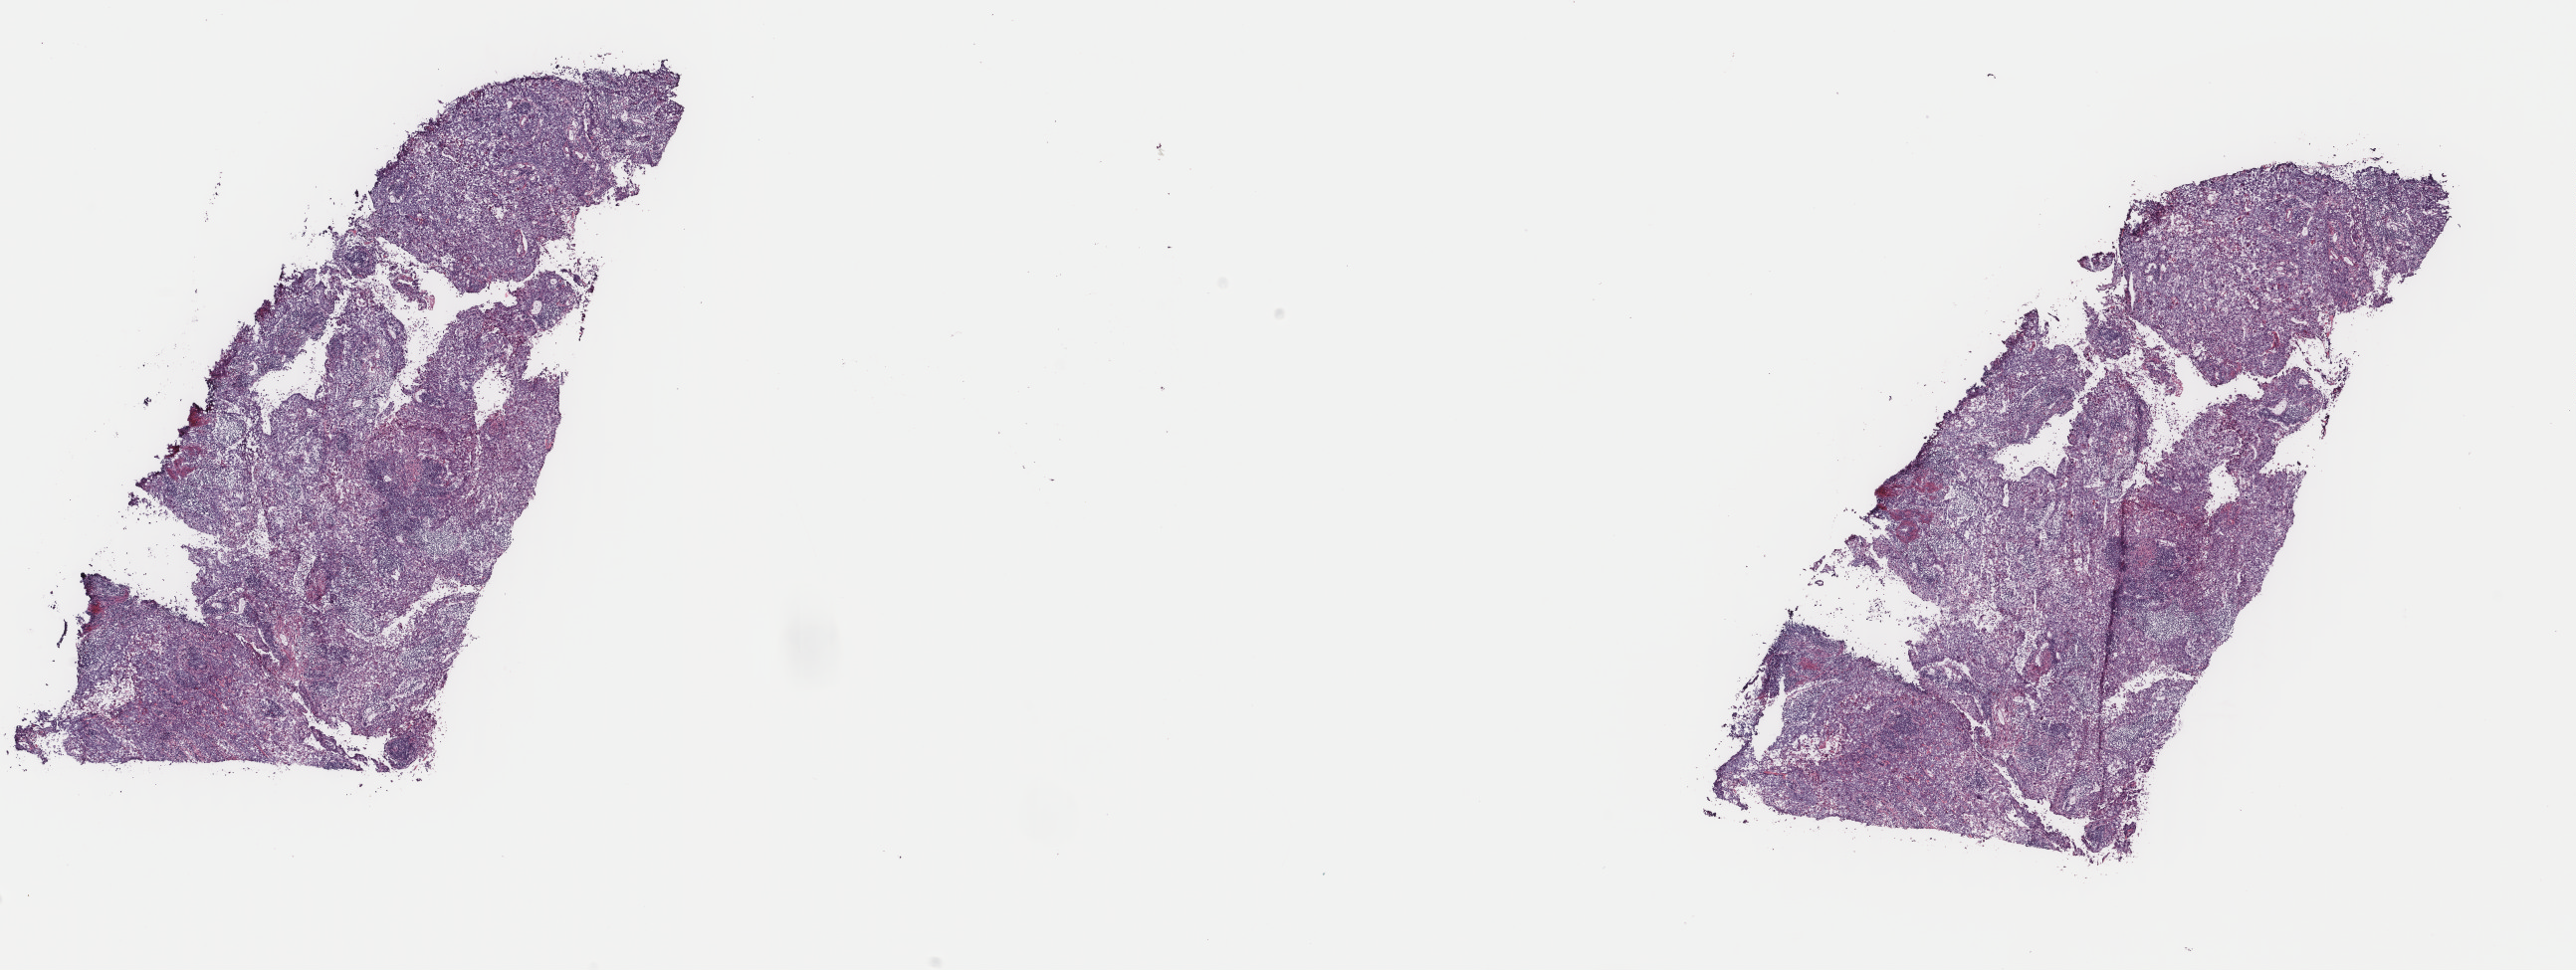
Hematoxylin and eosin (H&E) stained whole-slide image, whole scanned area (about 20.5 x 7.7 mm, acquisition: 40x scan) shown as a low-resolution overview; frozen section from the top of the tissue portion; bladder, primary tumour sample. Male patient; age at initial diagnosis 78 years. Histologic grade: high grade. Slide review estimates, as recorded: tumour cells 97%, tumour nuclei 70%, normal cells 0%, stromal cells 0%, necrosis 3%. Infiltration values recorded for this section: lymphocyte infiltration 13%, monocyte infiltration 0%, neutrophil infiltration 1%.
AJCC pathologic stage: IV. Histologic diagnosis: Transitional cell carcinoma. Lymph nodes positive (case pathology): 3 of 31 examined.